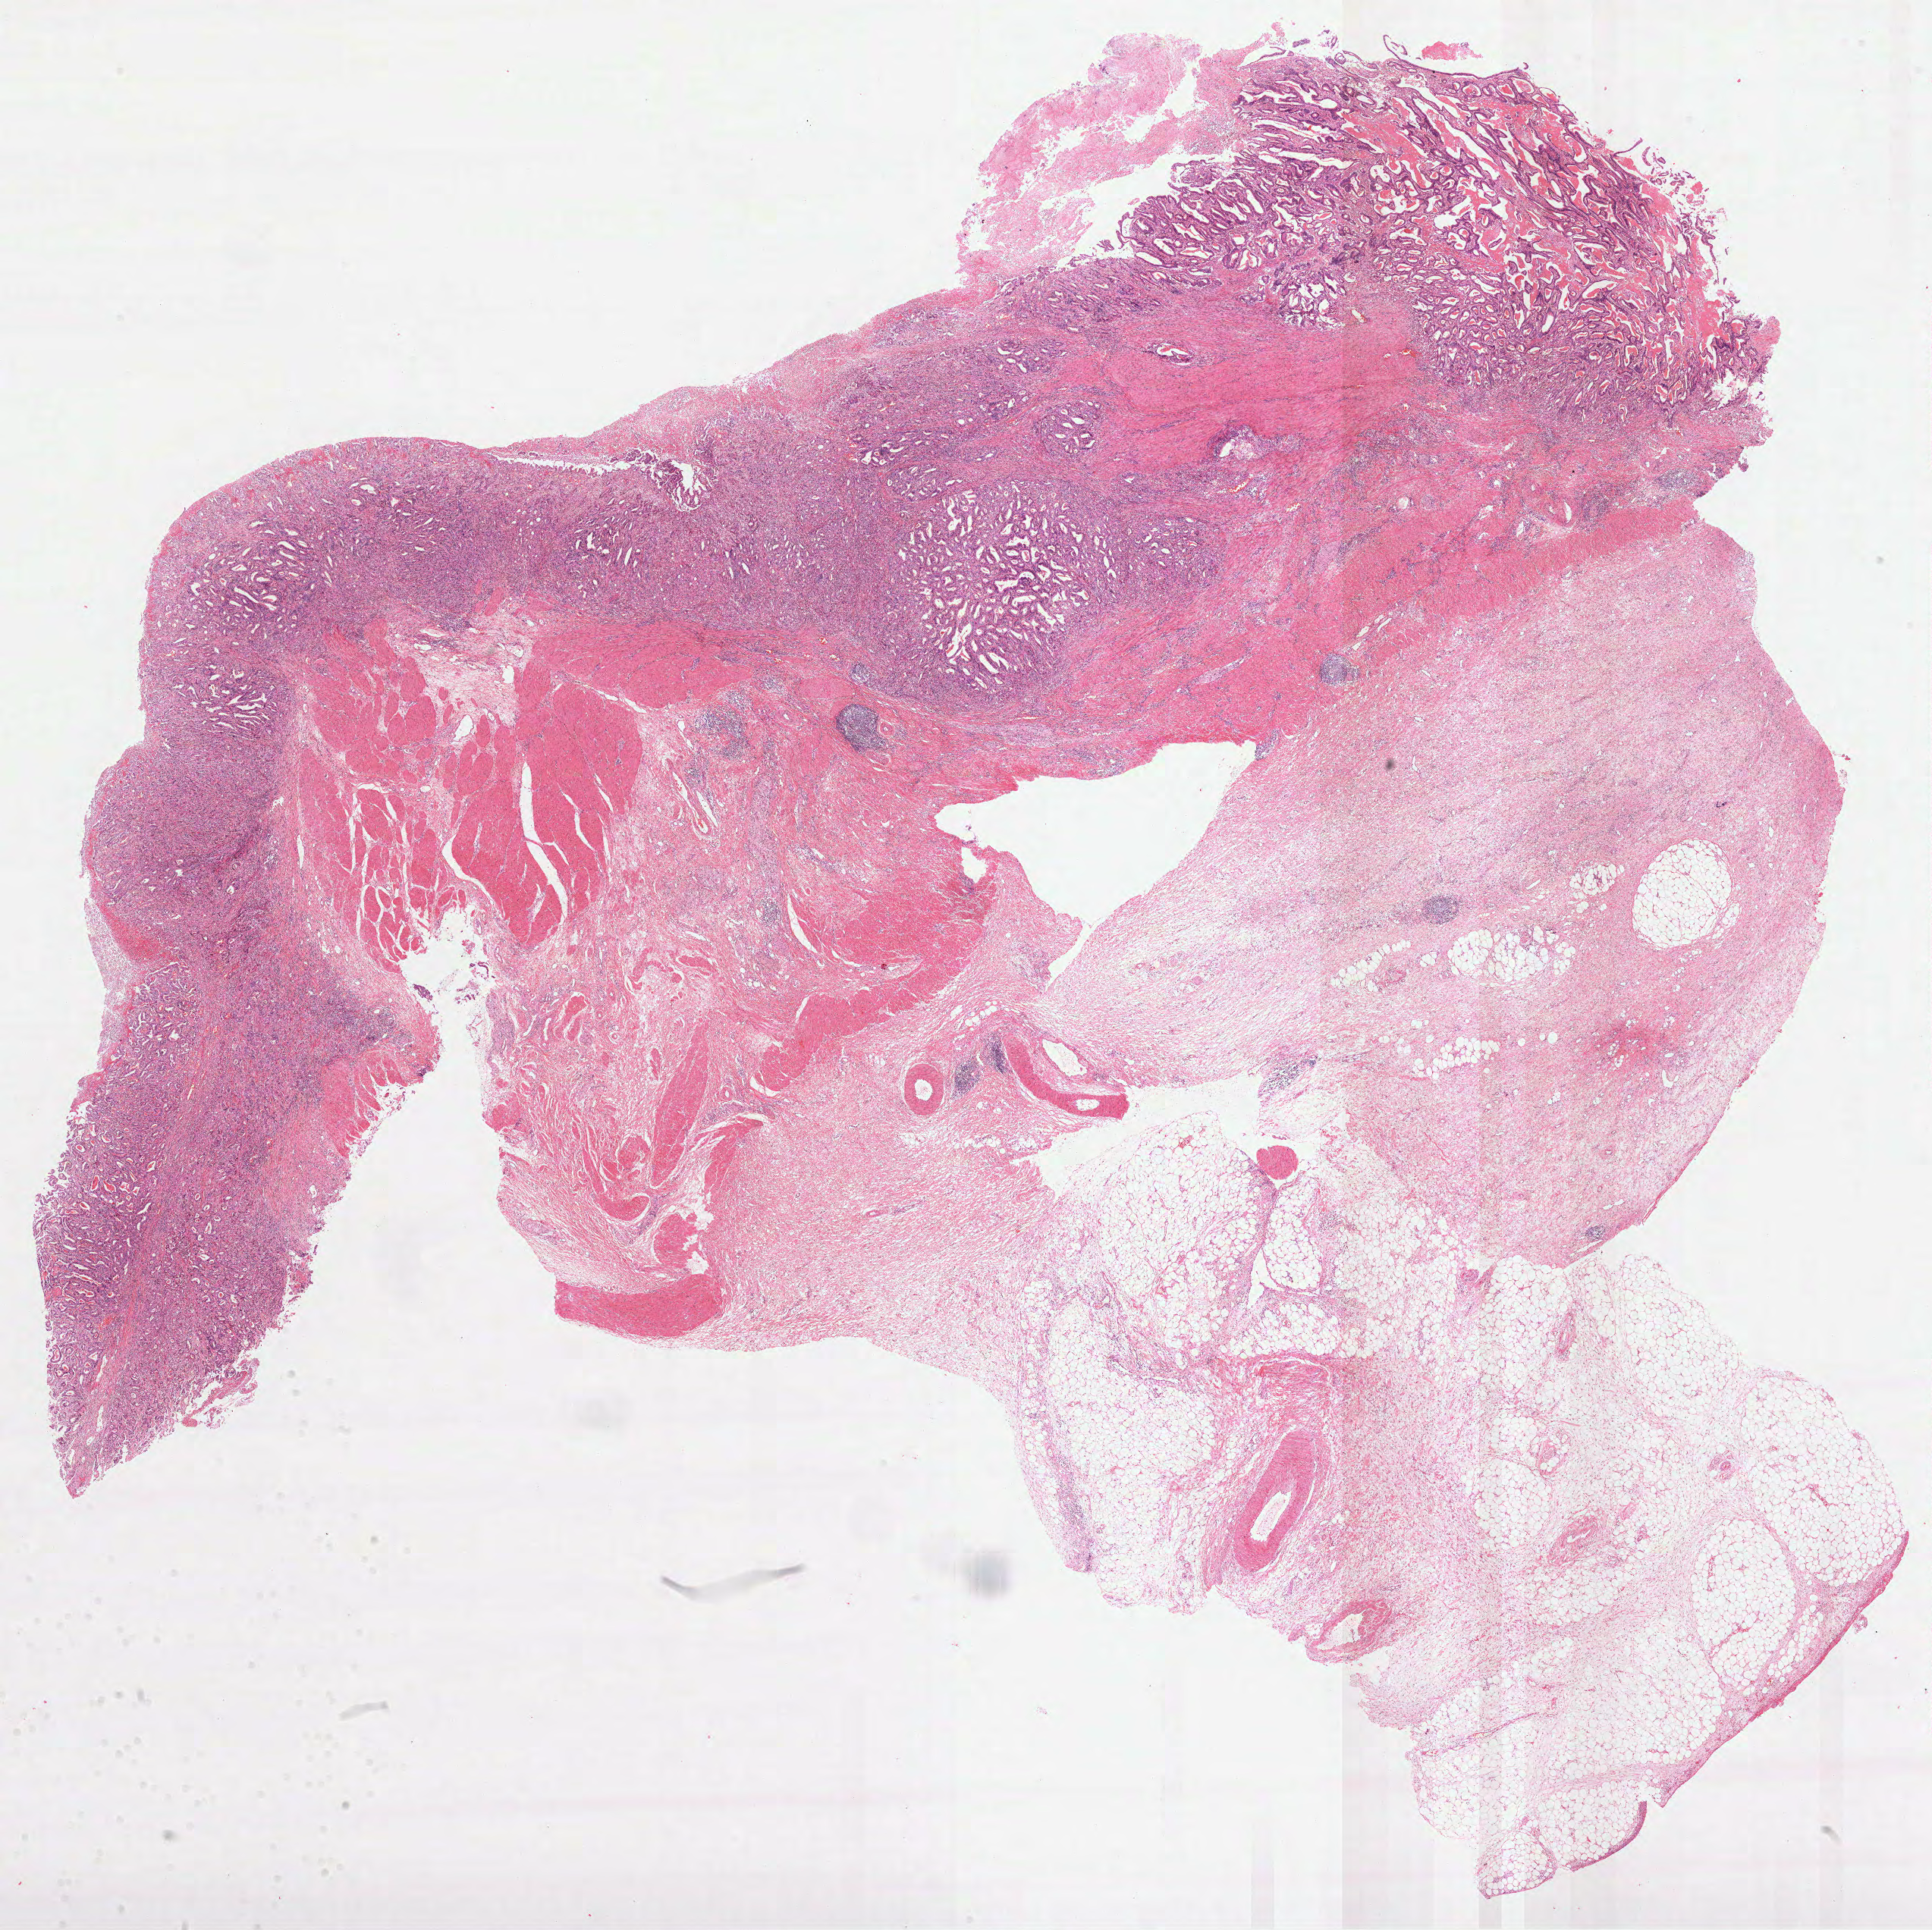
H&E whole-slide image, shown as a low-resolution overview of the whole scanned area (about 20.5 x 20.5 mm, from a 40x scan); FFPE section; primary tumour sample from the stomach. Female, age 64 years at initial diagnosis. Histologic grade: G3 (poorly differentiated).
* TNM: T3 N0 M0
* lymph nodes positive (case pathology): 0 of 15 examined
* AJCC pathologic stage: IIA
* pathologic diagnosis: Adenocarcinoma, NOS (gastric antrum)